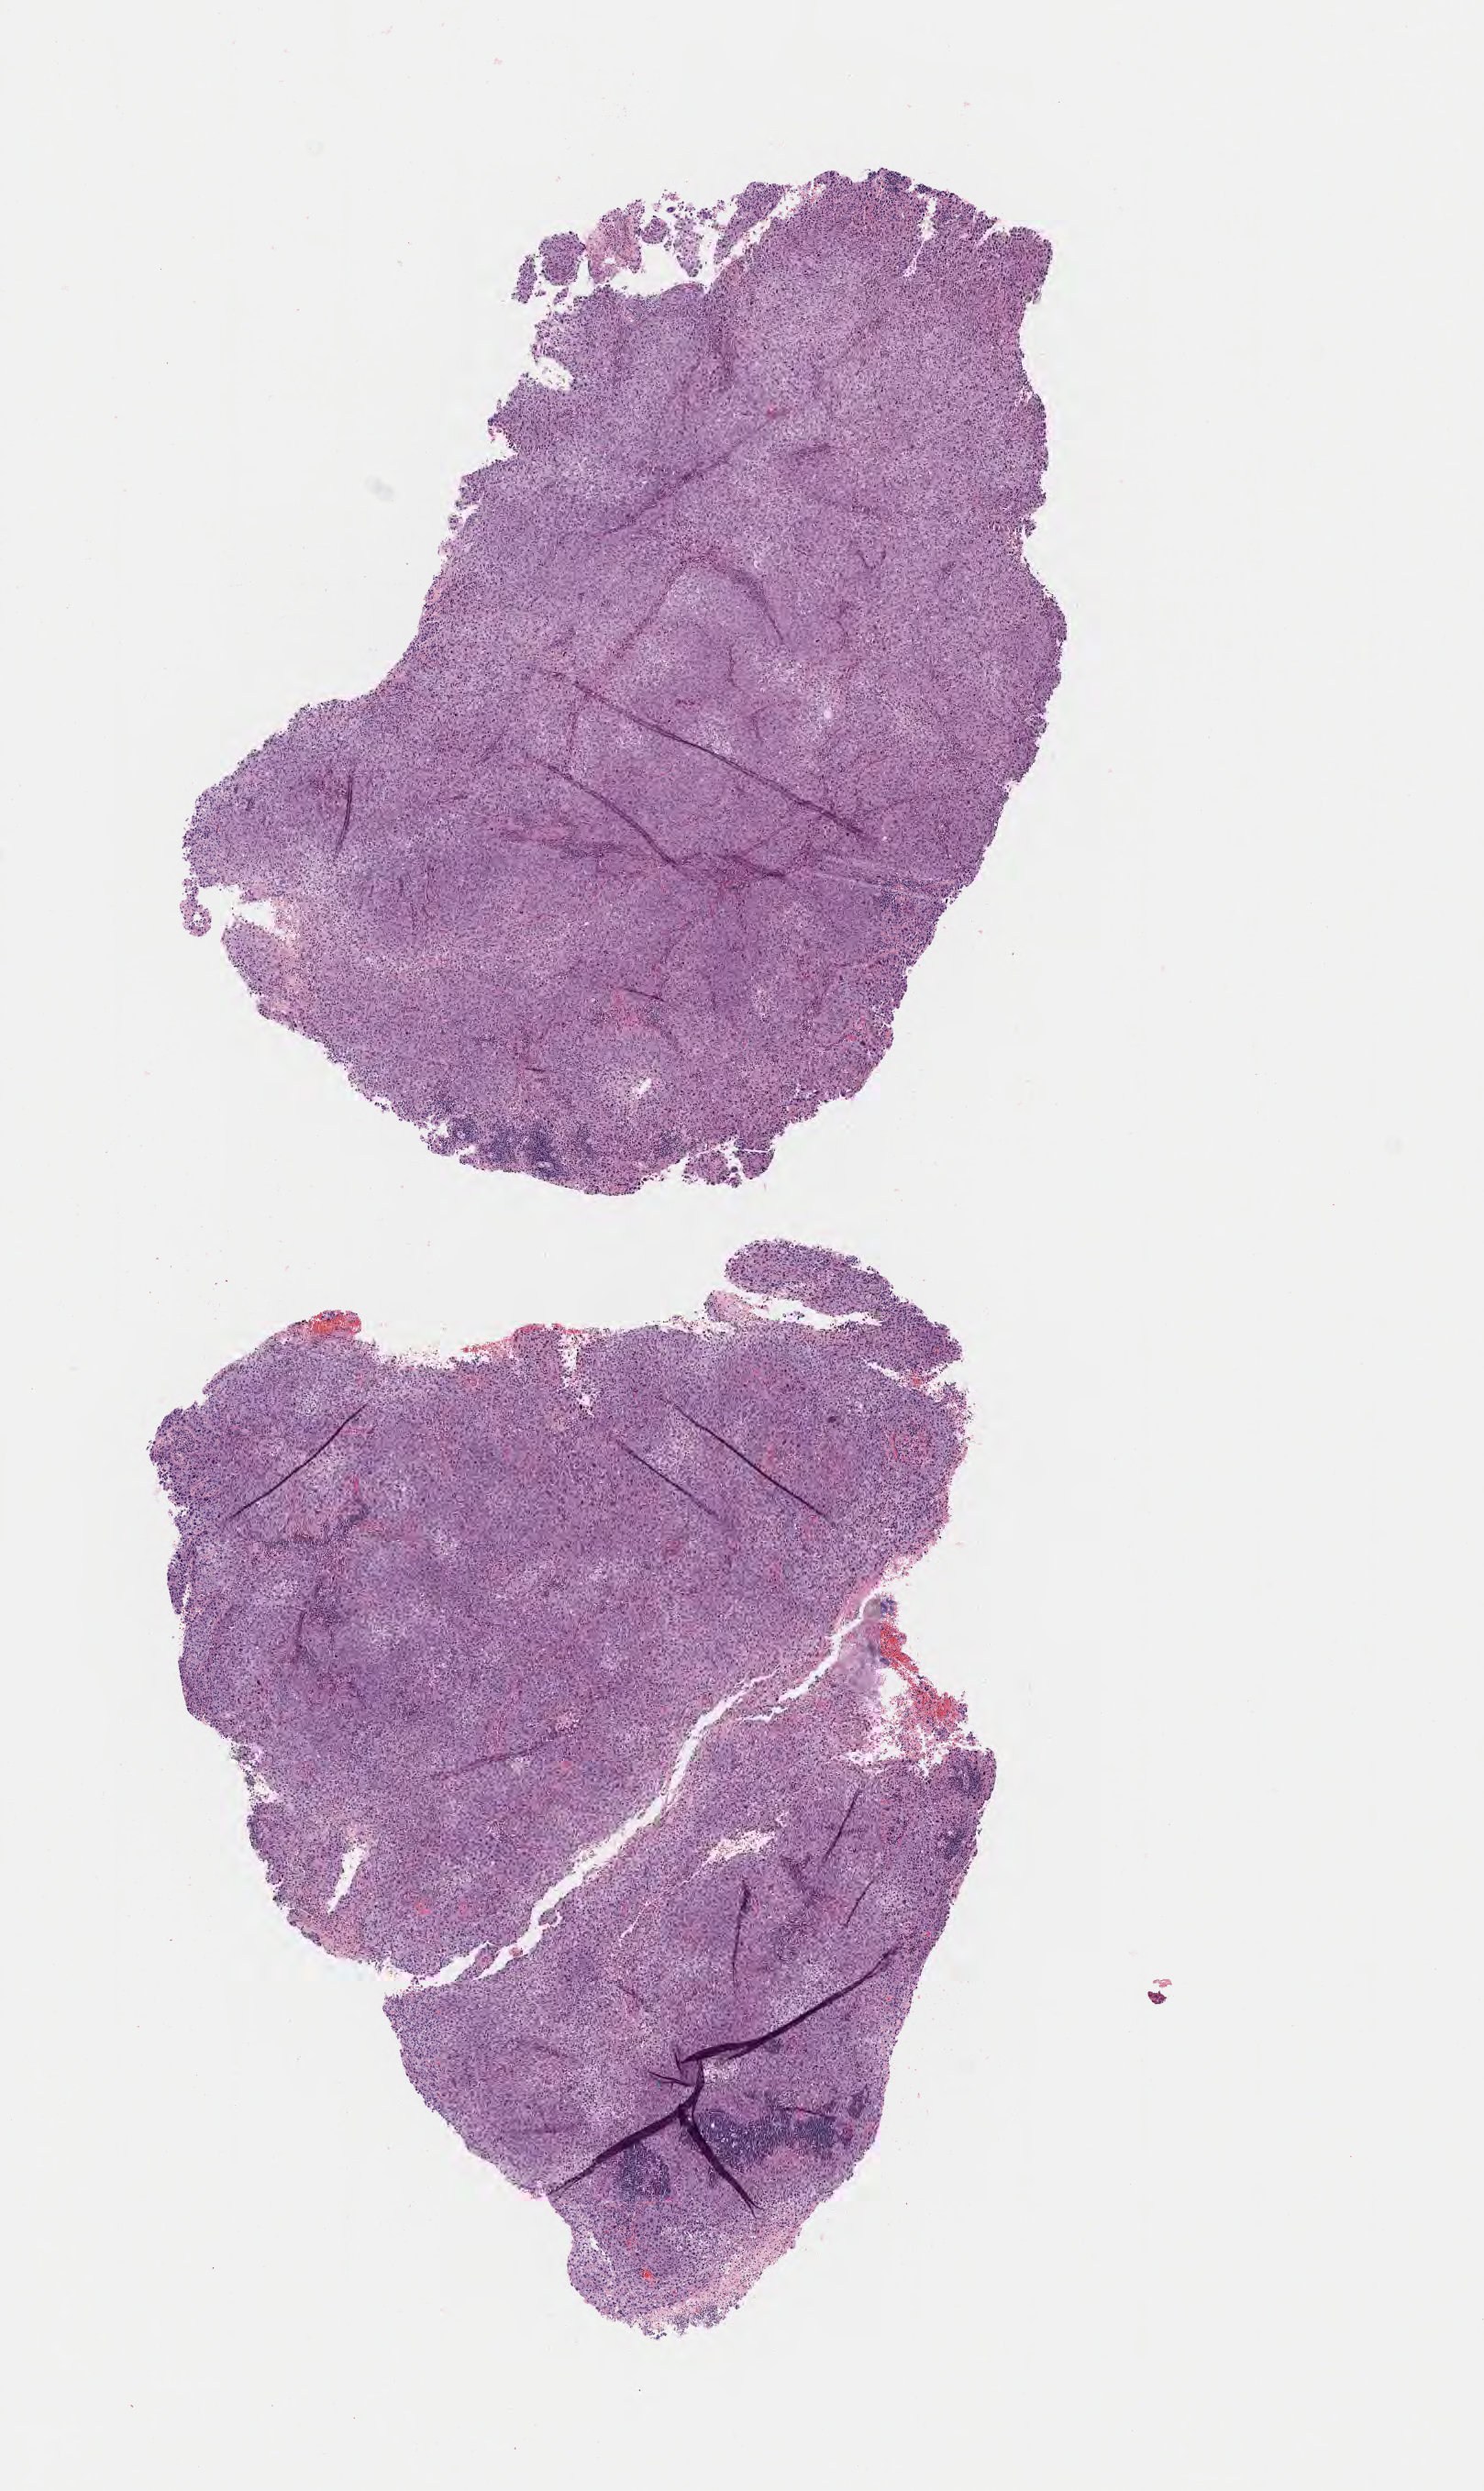
Digitized hematoxylin and eosin (H&E)-stained section — low-resolution overview of the scanned area, about 6.5 x 11.0 mm. Specimen: tumor tissue. Anatomic site: cervix. Patient: female, age 45 years.
- histologic diagnosis: Squamous cell carcinoma, large cell, nonkeratinizing, NOS